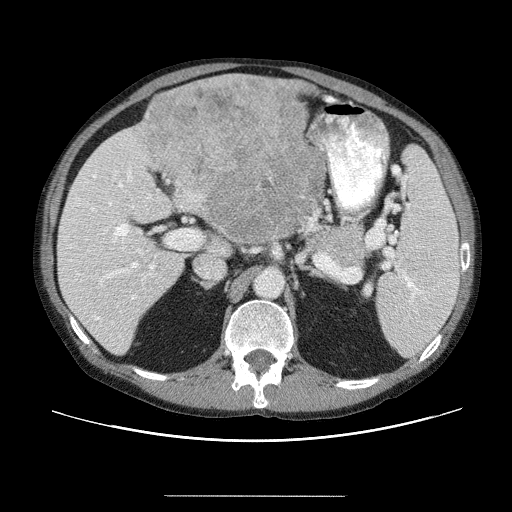
Contrast-enhanced abdominal CT (liver protocol), one axial slice. Position 24 of 69 along the scan axis. Soft-tissue window (W 400 / L 40 HU). 2.5 mm slice thickness. 512 × 512 image matrix. From the clinical record (not read from this slice): diagnosis: hepatocellular carcinoma (patient treated with transarterial chemoembolisation; whether this scan precedes or follows treatment is not stated here); TNM stage (as recorded): Stage-IVB; Child-Pugh class: B; tumour differentiation: poorly differentiated.
Annotated regions visible in this slice (semi-automatically segmented with operator editing):
- liver parenchyma outside the tumour (the mass and vessels are separate outlines, so this box may not span the whole liver): bounding box (x1, y1, x2, y2) in pixels: (56, 82, 309, 352)
- mass: (130, 76, 328, 251)
- liver vessels: (70, 160, 160, 337)